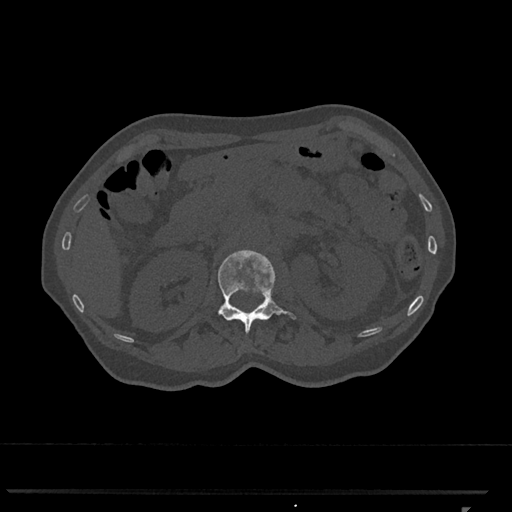
CT including the spine, one axial slice; position 401 of 793 along the scan axis; bone window (W 1800 / L 400 HU); 0.5 mm slice thickness; 512 × 512 image matrix. Female patient, age 62 years. Case-level facts recorded for this patient, not image findings: primary cancer: renal.
Structures marked on this image (semi-automatically segmented with operator editing):
- L1 vertebra: box from (x=218, y=250) to (x=297, y=334) px